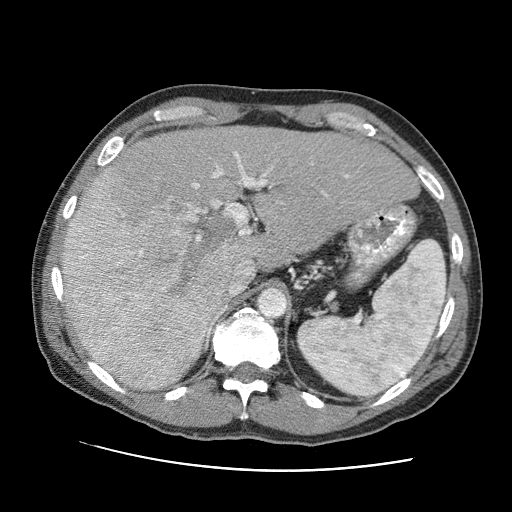
Contrast-enhanced abdominal CT (liver protocol), one axial slice; slice 60 of 95 in the series (ordered by position); one of 2 acquisitions stored at this slice position; soft-tissue window (W 400 / L 40 HU); 2.5 mm slice thickness; 512 × 512 image matrix, field of view 360 × 360 mm. Case-level facts recorded for this patient, not image findings: diagnosis: hepatocellular carcinoma (patient treated with transarterial chemoembolisation; whether this scan precedes or follows treatment is not stated here); TNM stage (as recorded): Stage-IVA; Child-Pugh class: A; tumour differentiation: moderately differentiated.
Outlined on this slice (semi-automatic segmentation, software-assisted and operator-edited):
- liver parenchyma outside the tumour (the mass and vessels are separate outlines, so this box may not span the whole liver): bounding box [x1, y1, x2, y2] px = [62, 126, 418, 390]
- mass: [61, 172, 245, 387]
- liver vessels: [192, 152, 349, 318]